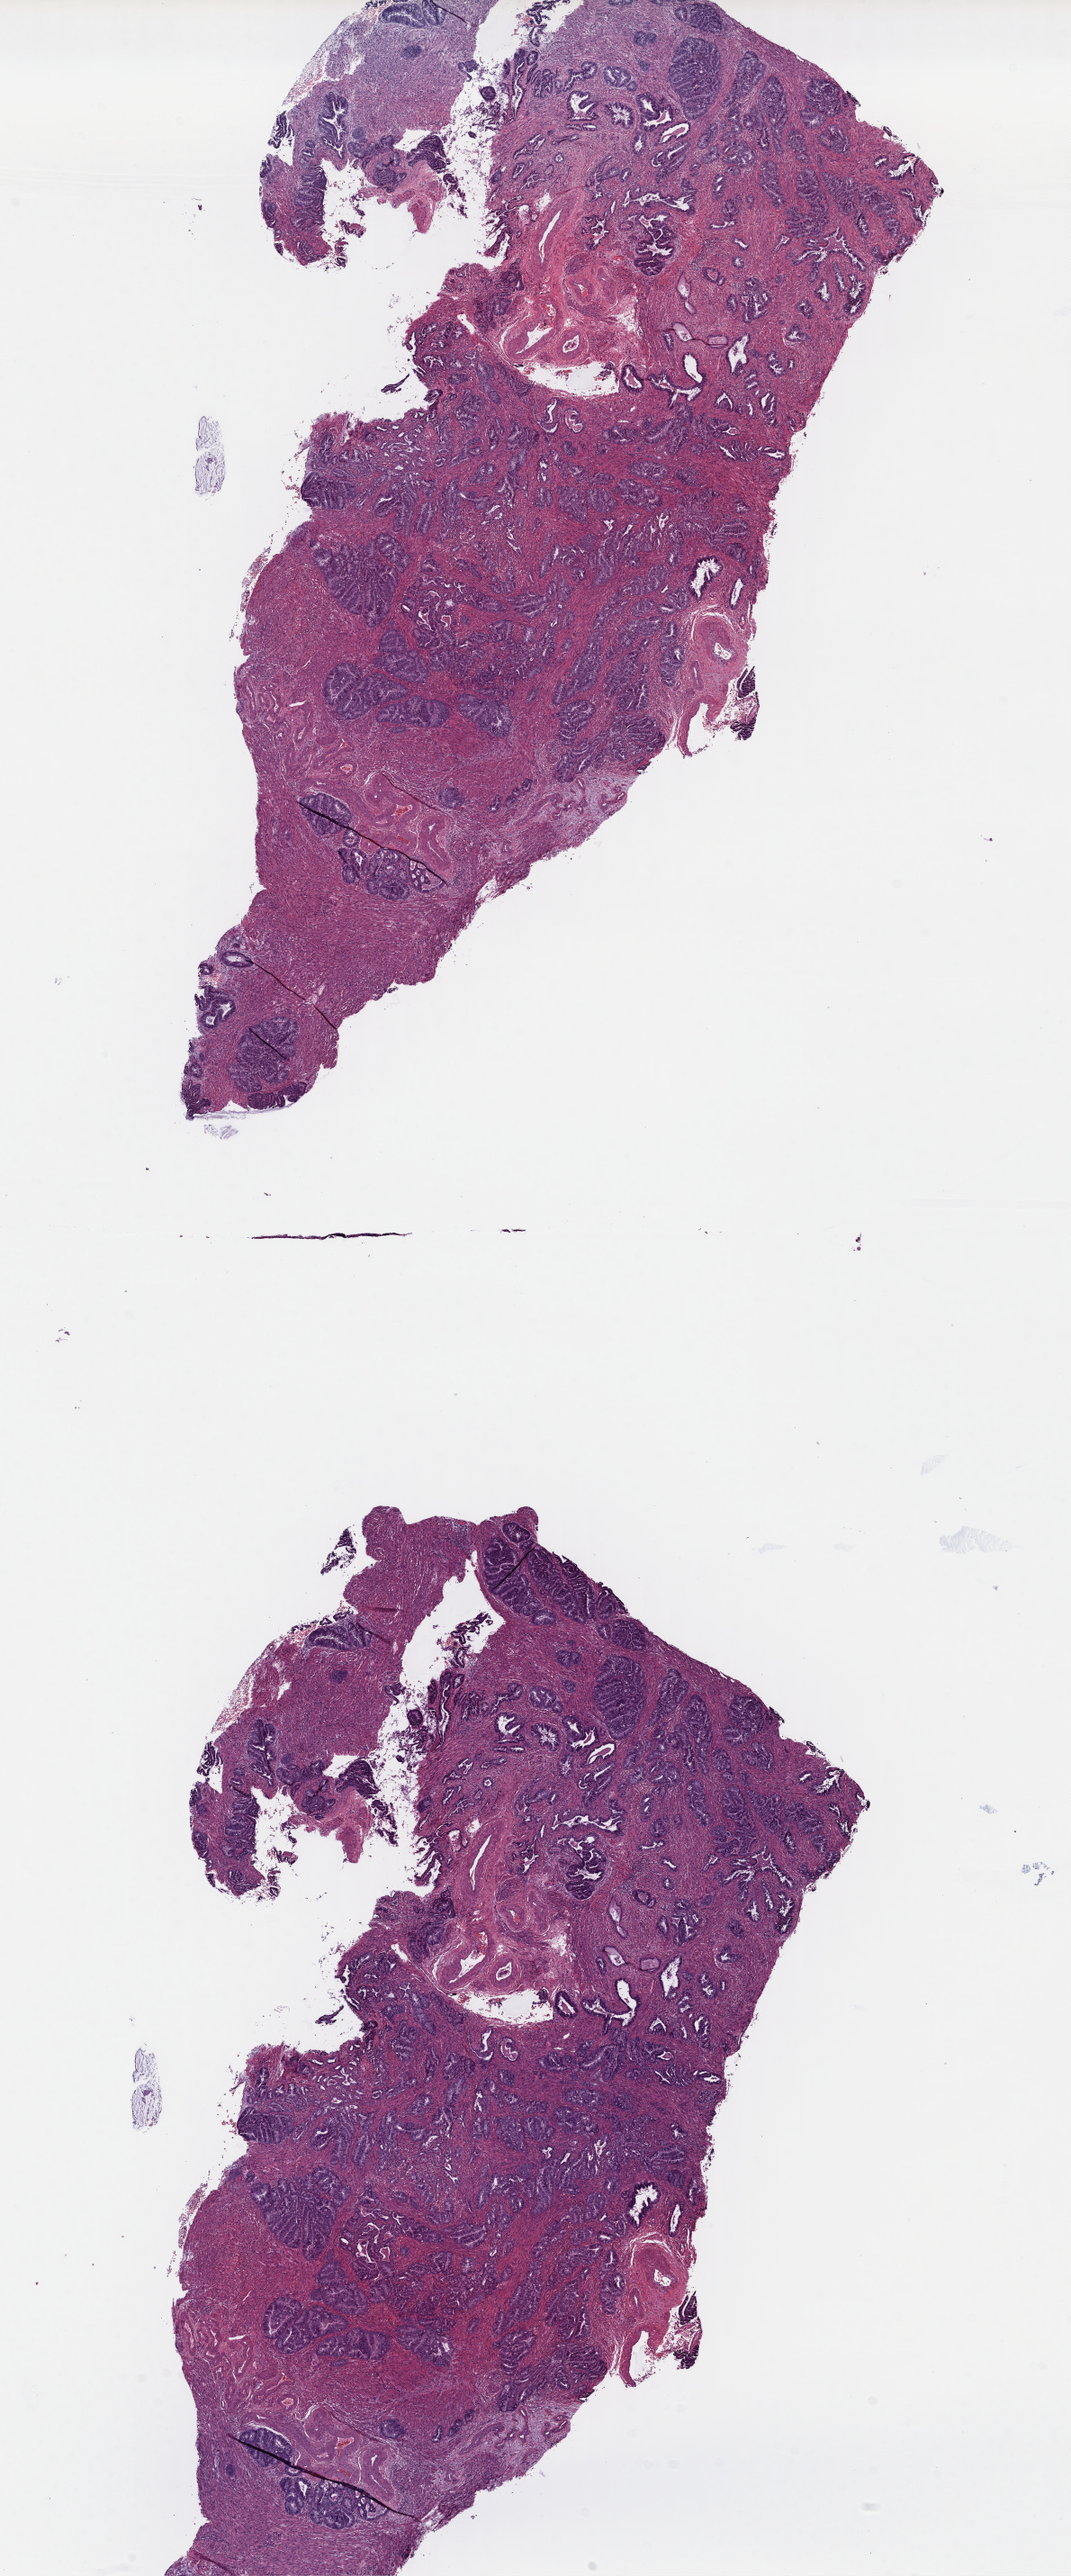
Digitized H&E-stained tissue section (whole slide) — shown as a low-resolution overview of the whole scanned area (about 9.4 x 22.5 mm). FFPE section. Primary tumour sample from the uterus. Patient: female, age at initial diagnosis 75 years.
Histologic diagnosis: Endometrioid adenocarcinoma, NOS (endometrium).